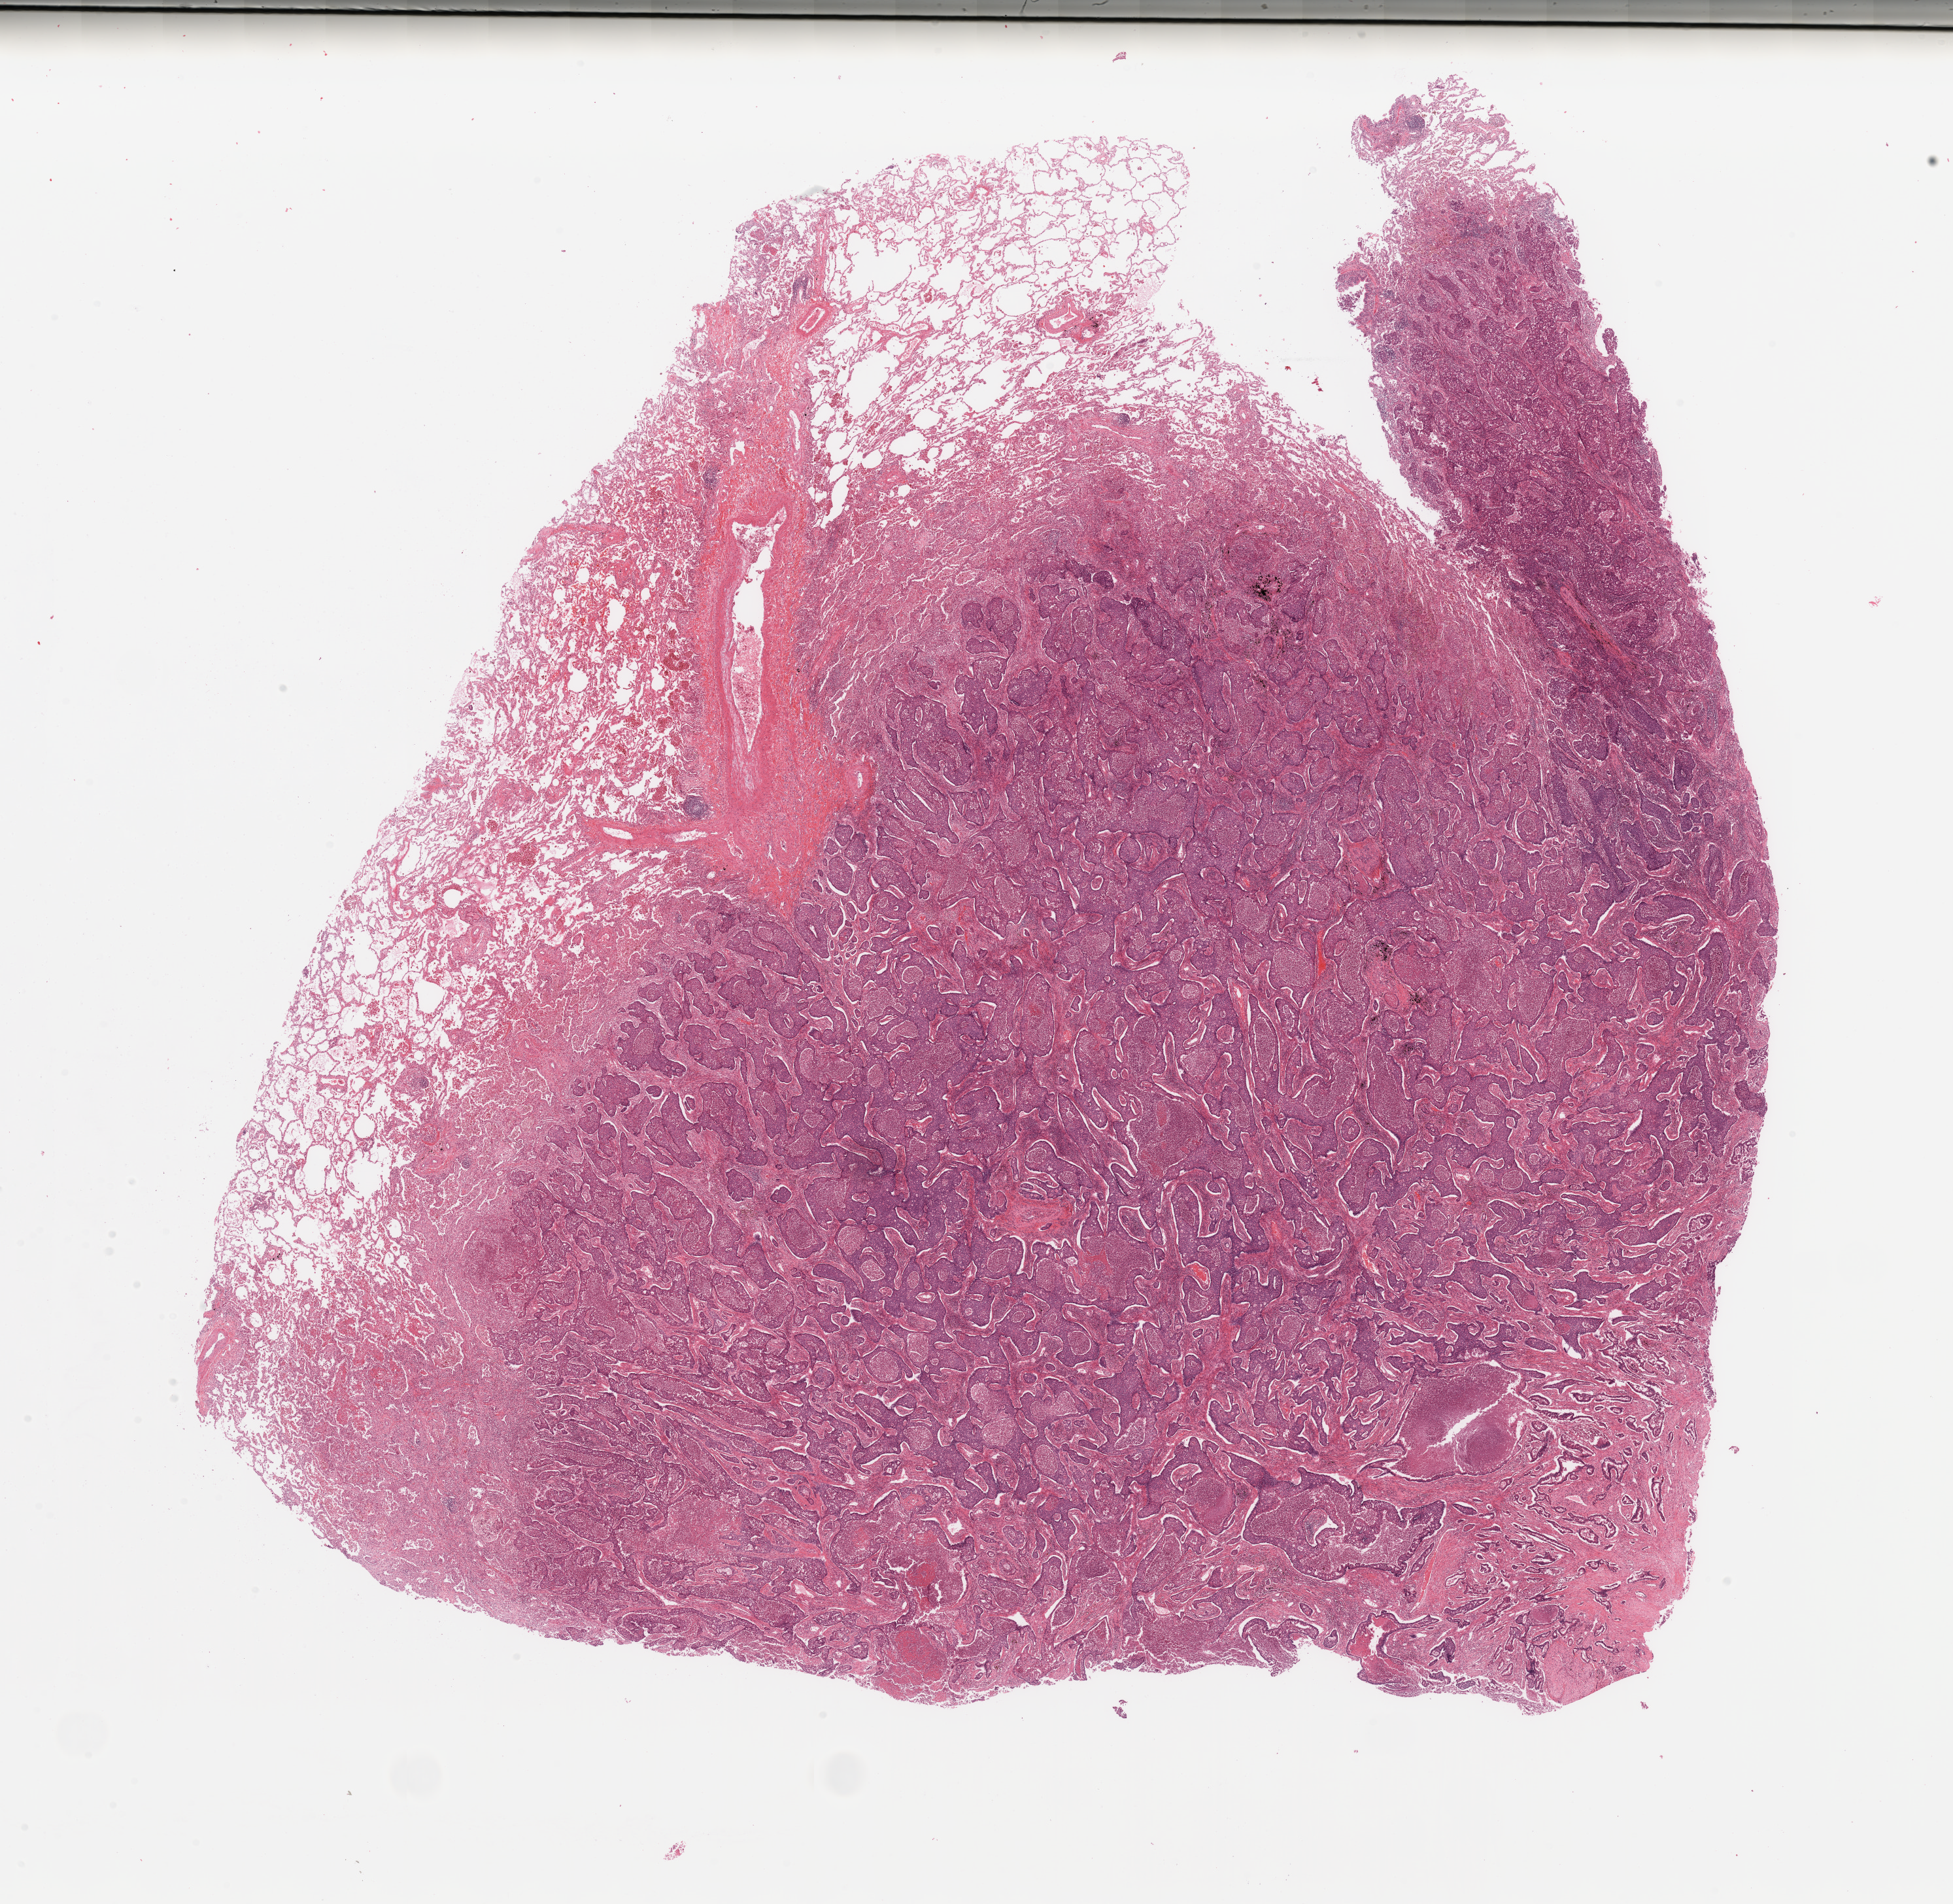
Digitized H&E tissue section (whole slide), whole scanned area (about 23.6 x 23.0 mm, slide scanned at 20x) shown as a low-resolution overview, tumour tissue sample, lung. Patient: male, age 58 years.
Histologic diagnosis: Adenocarcinoma, NOS.